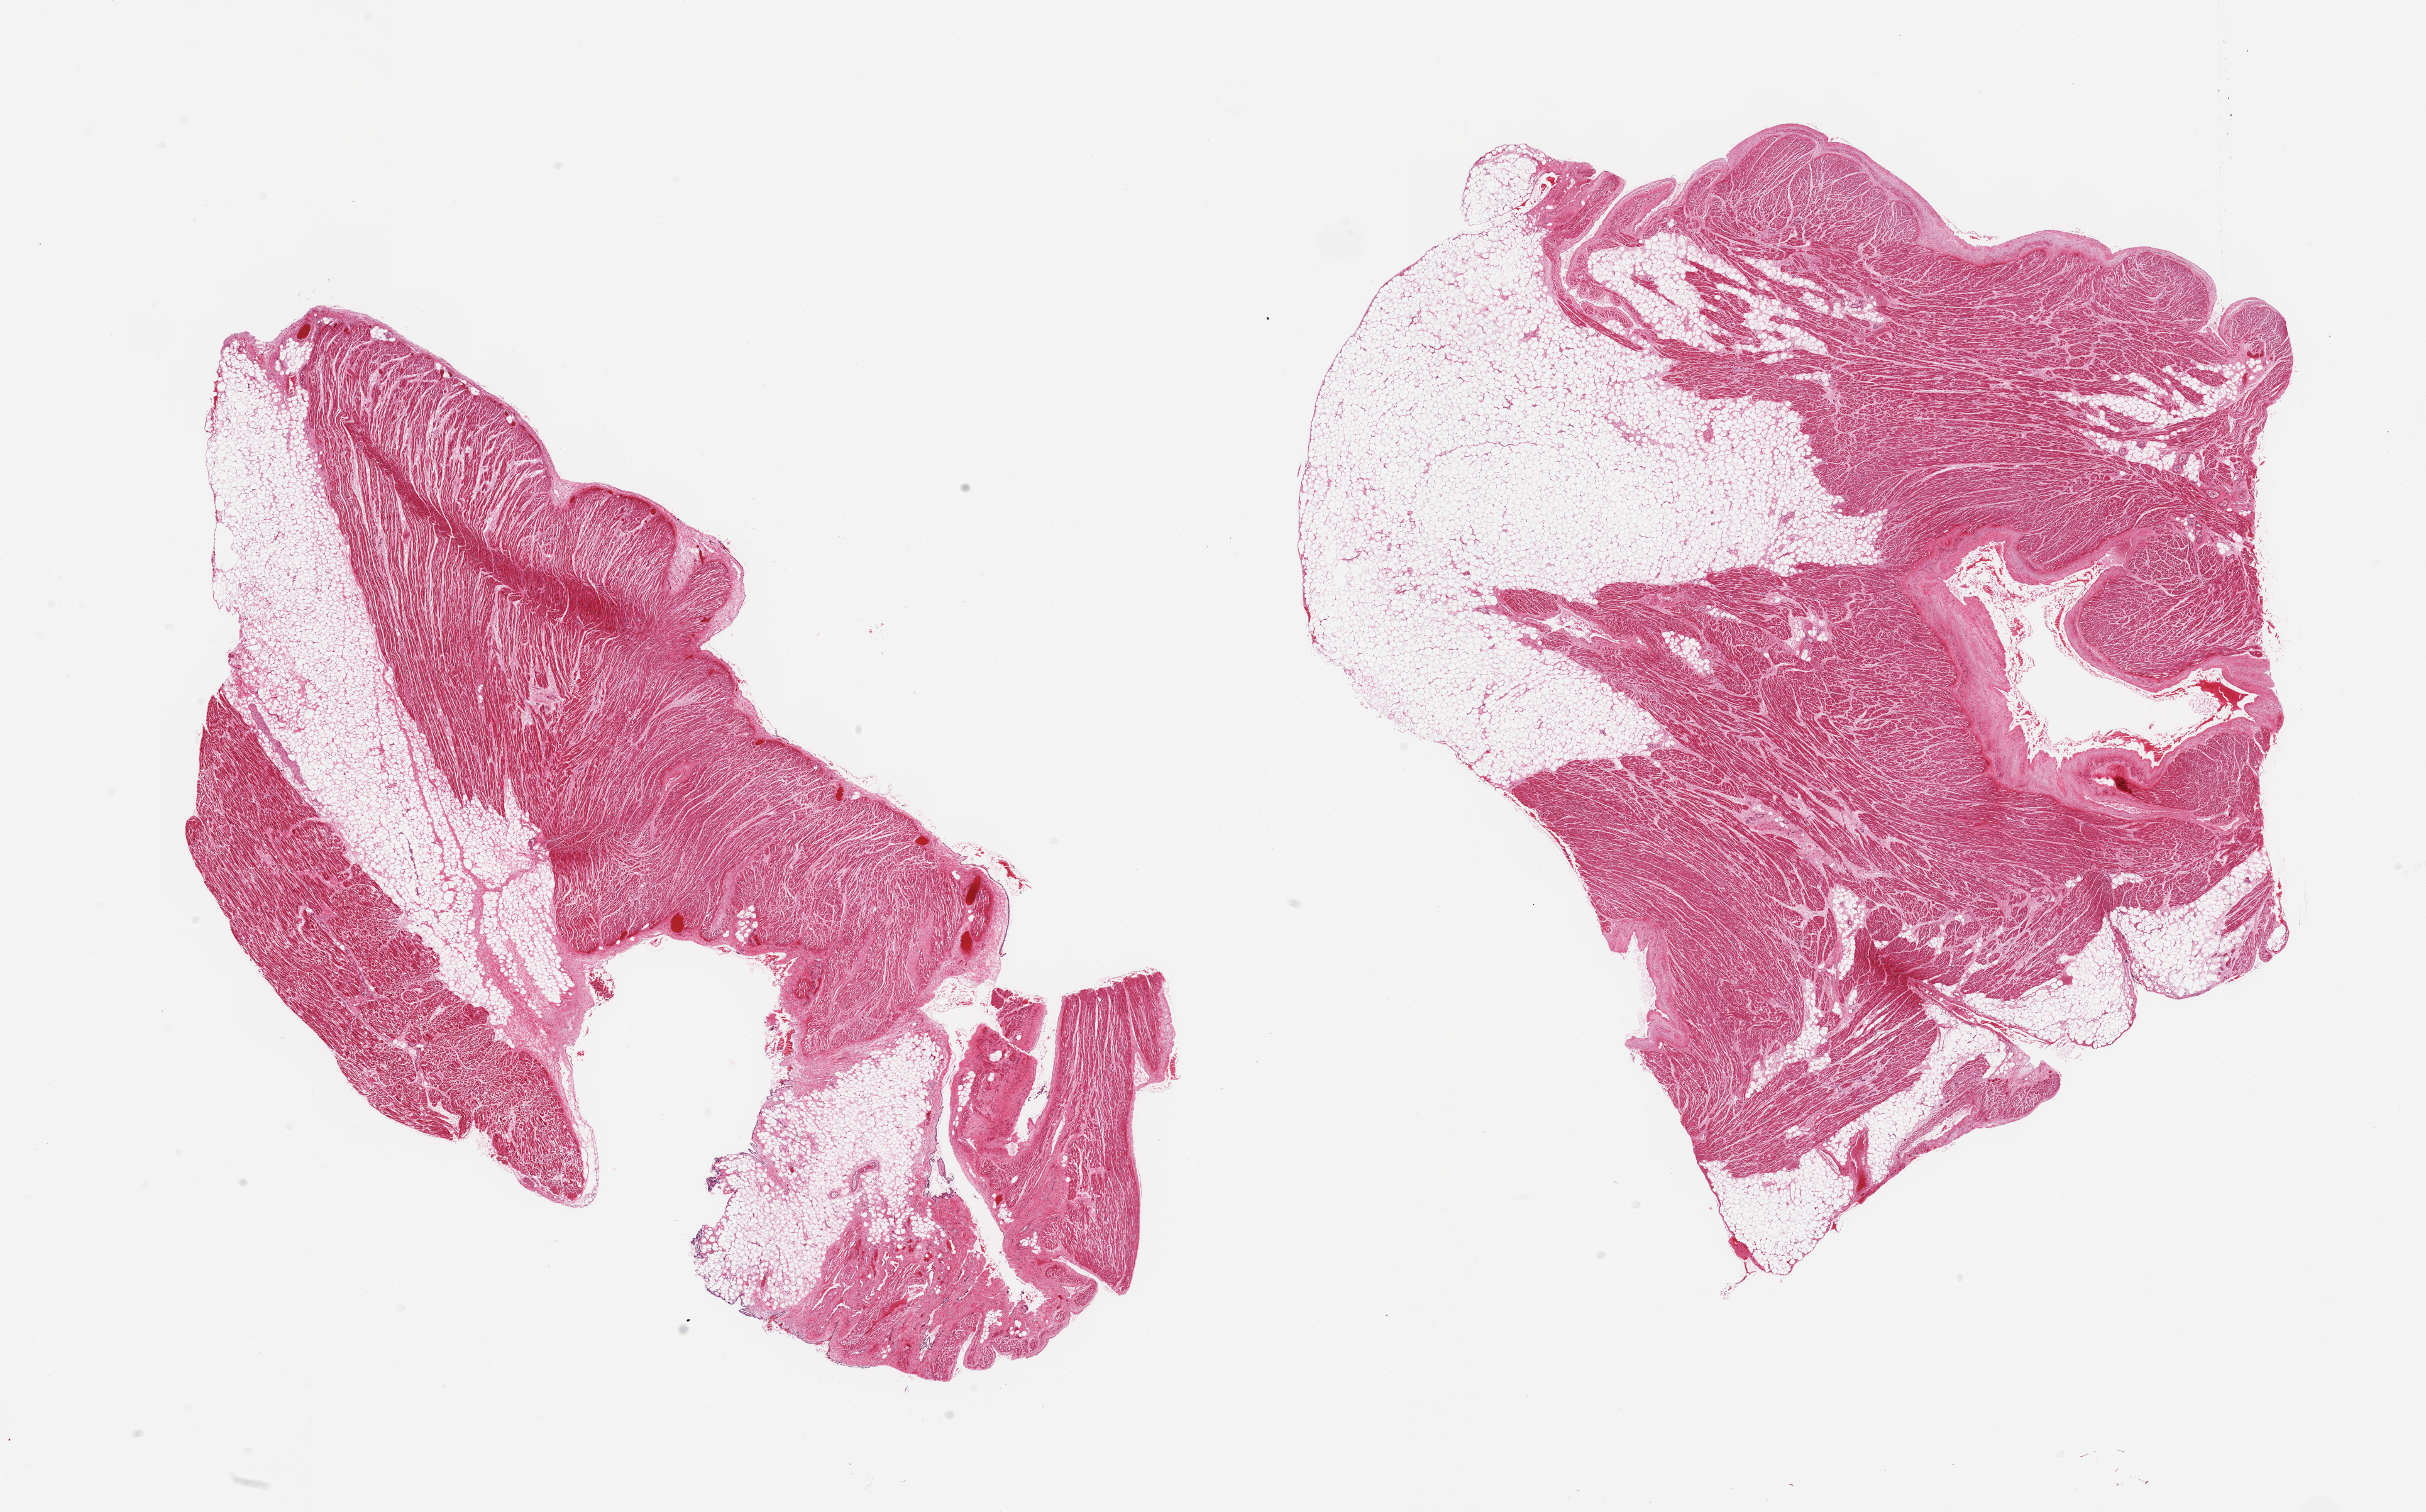
Whole-slide image, haematoxylin and eosin stain, low-resolution overview of the scanned area, about 30.5 x 19.0 mm; PAXgene-fixed paraffin-embedded (PFPE) section; target tissue: auricular appendage; tissue donor sample. Donor sex: male.
* pathologist's review note for this sample: 2 pieces; fibromuscular tissue and ~50% internal/external fat